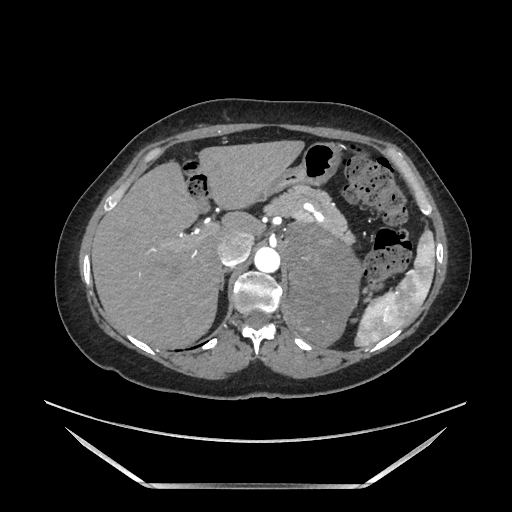
Contrast-enhanced abdominal CT, one axial slice; slice 125 of 205 in the series (ordered by position); soft-tissue window (W 400 / L 40 HU); 1.25 mm slice thickness; 512 × 512 image matrix, field of view 440 × 440 mm. Female patient. From the clinical record (not read from this slice): diagnosis: adrenocortical carcinoma; tumour side: left adrenal; tumour size at pathology: 12.5 cm; Ki-67 index: 39 %.
Structures marked on this image (semi-automatic segmentation, software-assisted and operator-edited):
- mass: bounding box <286,221,361,345> (left, top, right, bottom; pixels)